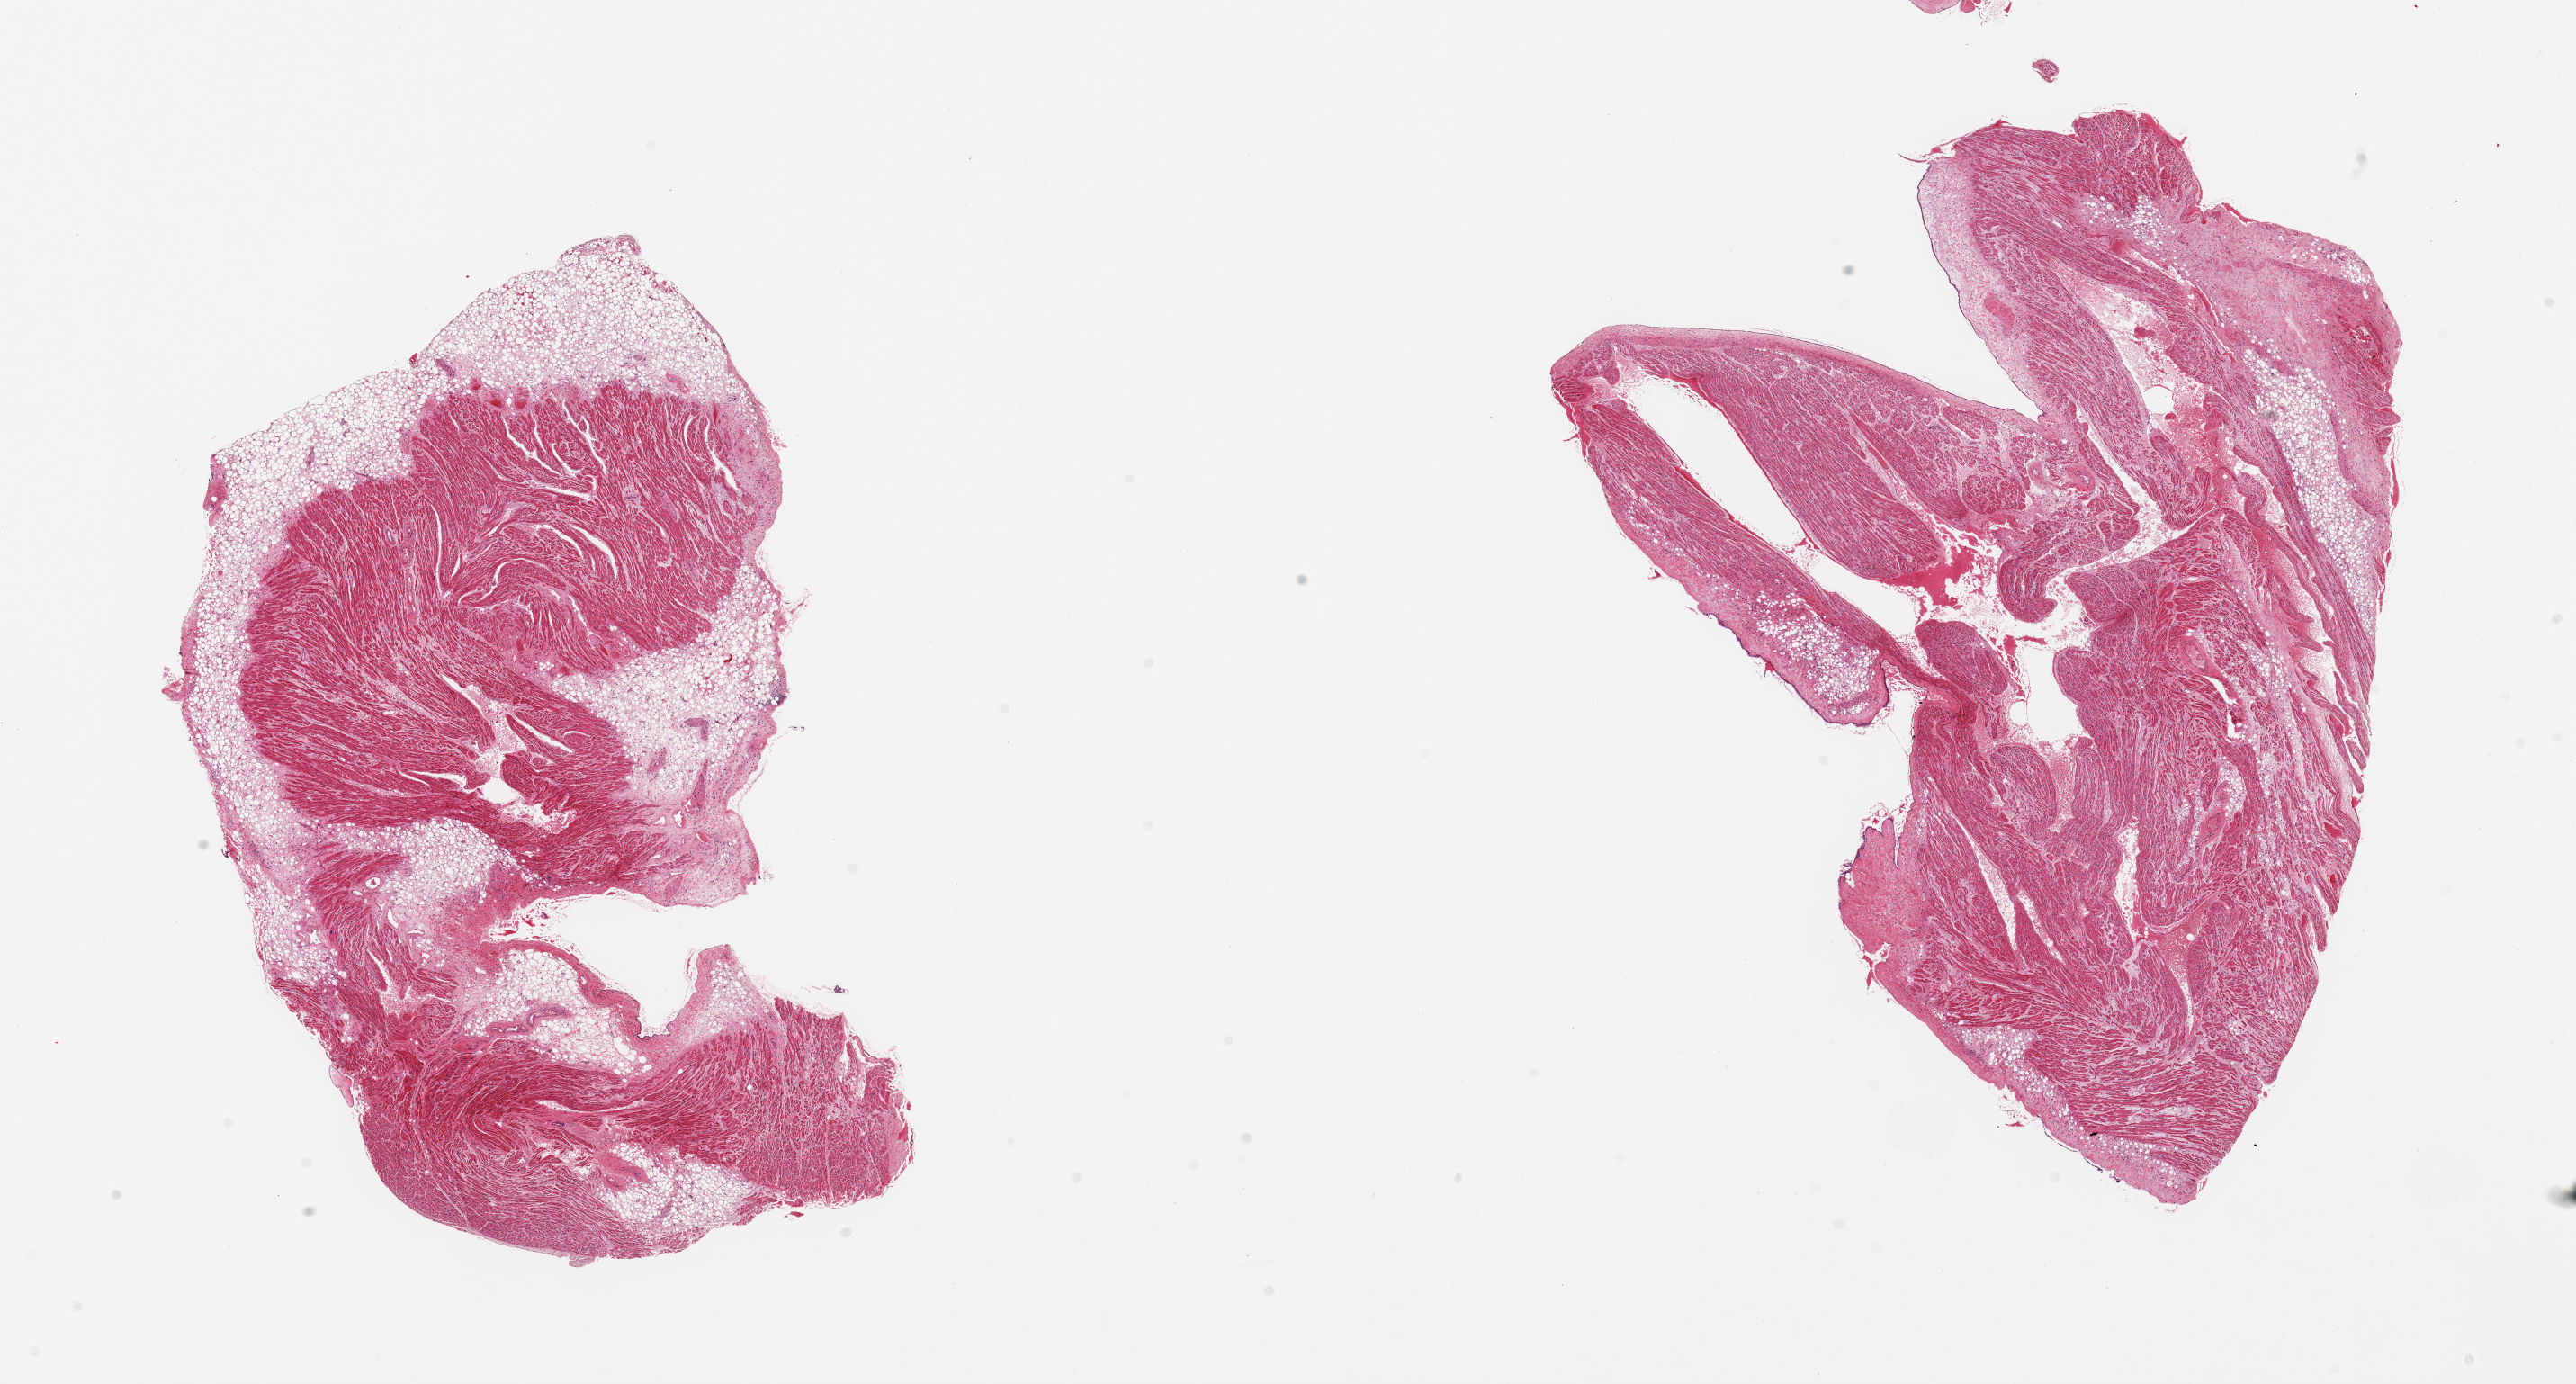
Hematoxylin and eosin (H&E) whole-slide image — whole scanned area (about 22.6 x 12.2 mm, acquisition: 20x scan) shown as a low-resolution overview; PAXgene-fixed paraffin-embedded (PFPE) section; target tissue: auricular appendage; tissue donor sample.
* review note (as recorded): 2 pieces; 40 & 10% fibroadipose content